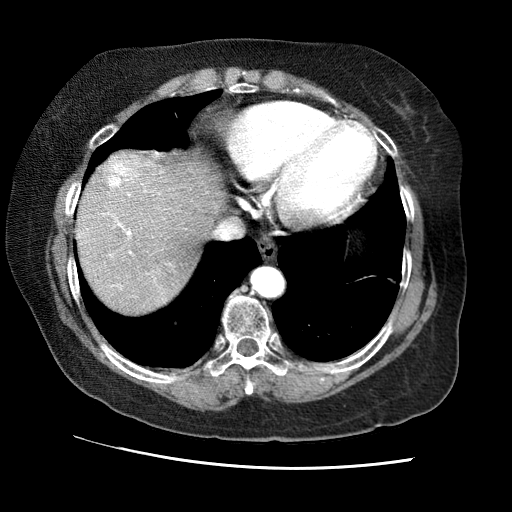
Contrast-enhanced abdominal CT (liver protocol), one axial slice. Slice 61 of 65 in the series (ordered by position). Soft-tissue window (W 400 / L 40 HU). 512 × 512 image matrix, field of view 340 × 340 mm. From the clinical record (not read from this slice): diagnosis: hepatocellular carcinoma (patient treated with transarterial chemoembolisation; whether this scan precedes or follows treatment is not stated here); TNM stage (as recorded): Stage-II; Child-Pugh class: A; tumour nodularity: multinodular; tumour size: 2.5 cm.
Annotated regions visible in this slice (semi-automatic segmentation, software-assisted and operator-edited):
- abdominal aorta: box from (x=252, y=267) to (x=283, y=296) px
- liver parenchyma outside the tumour (the mass and vessels are separate outlines, so this box may not span the whole liver): (x=76, y=152)–(x=226, y=314)
- mass: (x=102, y=151)–(x=144, y=186)
- liver vessels: (x=78, y=152)–(x=158, y=286)